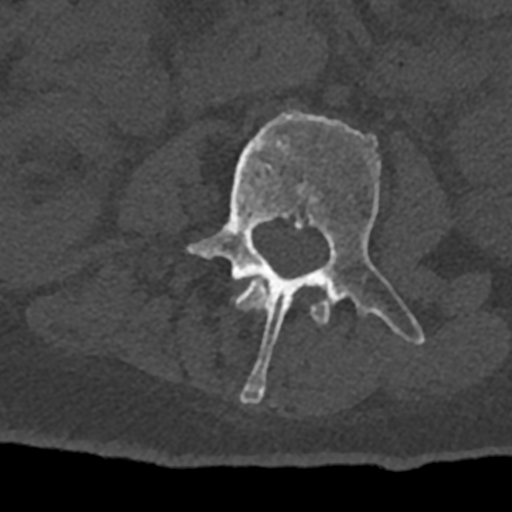
CT including the spine, one axial slice; position 322 of 797 along the scan axis; reconstruction kernel Br40s/3; 120 kVp; bone window (W 1800 / L 400 HU); 0.5 mm slice thickness; 512 × 512 image matrix. Patient: male, 74 years. Case-level facts recorded for this patient, not image findings: primary cancer: renal; vertebrae with lytic lesions (as recorded): T10, L1, L2, L3, L4, L5.
Outlined on this slice (semi-automatically segmented with operator editing):
- L2 vertebra: box from (x=232, y=281) to (x=329, y=325) px
- L3 vertebra: (x=185, y=110)–(x=425, y=403)